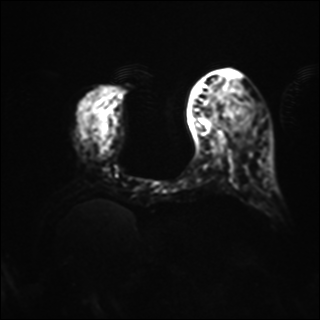
Breast MRI, one axial slice. Position 15 of 40 along the scan axis. Diffusion-weighted series; image 2 of 4 stored at this slice position (different b-values; order by instance number). 1.5 T. 4 mm slice thickness. 320 × 320 image matrix, field of view 320 × 320 mm. Female patient.
Annotated regions visible in this slice (expert manual segmentation):
- tumour on diffusion-weighted imaging: box from (x=242, y=103) to (x=251, y=115) px